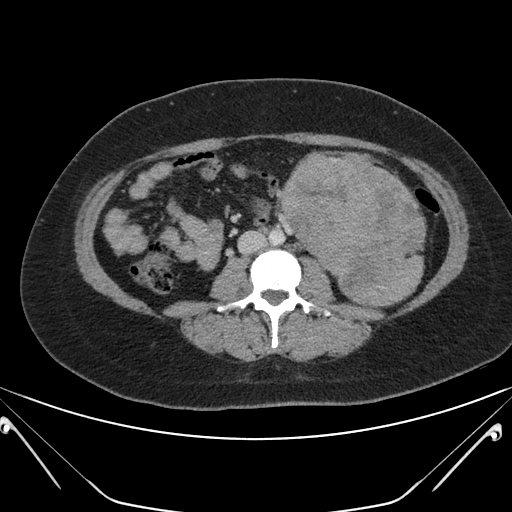
Contrast-enhanced abdominal CT, one axial slice. Position 89 of 168 along the scan axis. 120 kVp. Soft-tissue window (W 400 / L 40 HU). 3 mm slice thickness. 512 × 512 image matrix. Patient: female, 26 years. Case-level facts recorded for this patient, not image findings: diagnosis: adrenocortical carcinoma; tumour side: left adrenal; tumour size at pathology: 28 cm; Ki-67 index: 20 %; stage (as recorded): 2.
Structures marked on this image (semi-automatic segmentation, software-assisted and operator-edited):
- mass: bounding box [x1, y1, x2, y2] px = [284, 156, 423, 302]